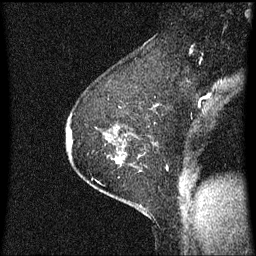
Breast MRI (dynamic contrast-enhanced), one sagittal slice. Slice 46 of 60 in the series (ordered by position). Dynamic contrast-enhanced series, image 2 of 3 at this slice position (ordered by acquisition). 1.5 T. TE 4.2 ms, TR 8.4 ms. 2 mm slice thickness. 256 × 256 image matrix, field of view 200 × 200 mm. Patient: female, 60 years.
Annotated regions visible in this slice (semi-automatically segmented with operator editing):
- analysis volume of interest (the breast-tissue region the enhancement analysis was run in; not a lesion): bounding box [x1, y1, x2, y2] px = [69, 66, 146, 193]
- tumour enhancement mask (voxels above the 70 % enhancement threshold inside the analysis volume of interest): [69, 134, 122, 163]